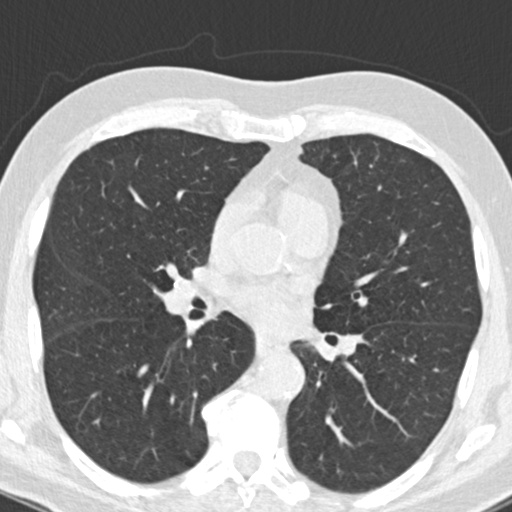
Chest CT (low-dose screening protocol), one axial image, second annual screen, lung window (W 1500 / L -600 HU), 2 mm slice thickness, slice 89 of 177 in the series. Male, age 66 years at enrolment. Current smoker at enrolment.
Lesion marked by an expert reader, bounding box (x1, y1, x2, y2) in pixels: (181, 315, 210, 341). Reader record for this screening exam (exam-level; its link to the box is not recorded): non-calcified nodule or mass ≥4 mm, right upper lobe, 5 × 4 mm, smooth margins, pre-existing on the prior screen: yes; interval growth: no. Official screen result: positive, other. Lung cancer was diagnosed 403 days after this screen: squamous cell carcinoma, NOS, right lower lobe, poorly differentiated (G3), stage IIA (AJCC 6th edition), 22 mm at pathology.